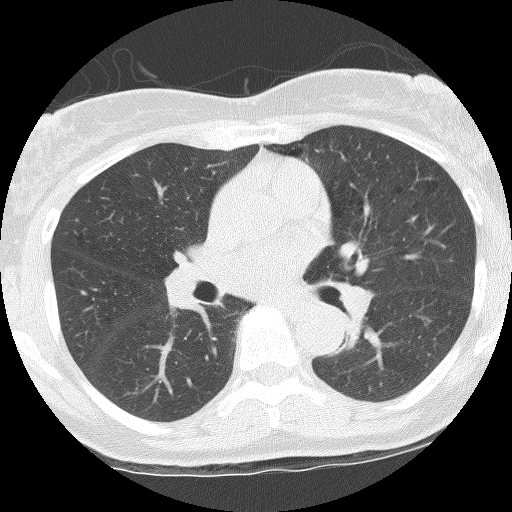
Axial slice from a low-dose chest CT screening exam. Third screening round (two years after baseline). Lung window (W 1500 / L -600 HU). 2.5 mm slice thickness. Female, age 62 years at enrolment. Former smoker at enrolment.
Expert reader's lesion annotation, box from (x=325, y=313) to (x=380, y=358) px. The screening reader recorded 3 non-calcified nodules or masses ≥4 mm on this exam (right upper lobe, left lower lobe, left upper lobe); which of them this box marks is not recorded. Official screen result: positive, other. Later outcome: lung cancer diagnosed 165 days after this screen — squamous cell carcinoma, NOS, left lower lobe, stage IIIB (AJCC 6th edition), 31 mm at pathology.